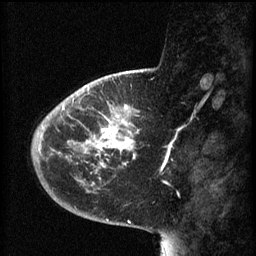
Breast MRI (dynamic contrast-enhanced), one sagittal slice. Position 18 of 60 along the scan axis. 3 images stored at this slice position (order not interpretable as contrast timing). 1.5 T. TE 4.2 ms, TR 8.1 ms. 256 × 256 image matrix, field of view 200 × 200 mm. Patient: female, 44 years.
Annotated regions visible in this slice (semi-automatically segmented with operator editing):
- analysis volume of interest (the breast-tissue region the enhancement analysis was run in; not a lesion): bounding box [x1, y1, x2, y2] px = [59, 110, 140, 169]
- tumour enhancement mask (voxels above the 70 % enhancement threshold inside the analysis volume of interest): [61, 110, 139, 167]